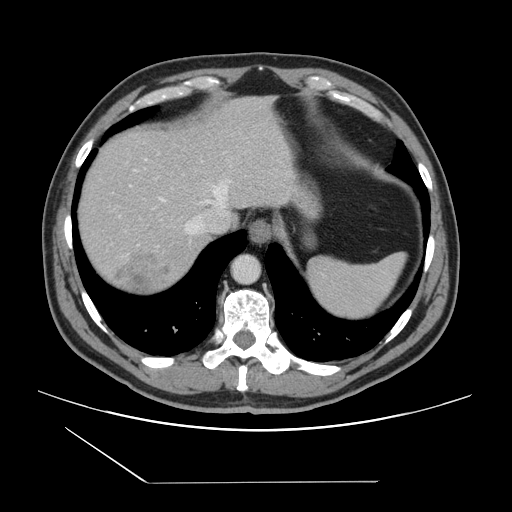
Contrast-enhanced abdominal CT, one axial slice. Position 123 of 157 along the scan axis. Intravenous contrast given. Soft-tissue window (W 400 / L 40 HU). 2.5 mm slice thickness. 512 × 512 image matrix, field of view 407 × 407 mm. Male patient, age 61 years. Case-level facts recorded for this patient, not image findings: diagnosis: colorectal cancer liver metastases, imaged before liver resection; multiple liver metastases: yes.
Outlined on this slice (expert manual segmentation):
- hepatic veins: bounding box [x1, y1, x2, y2] px = [160, 181, 228, 235]
- liver: [77, 96, 293, 296]
- planned liver remnant (the part of the liver to remain after resection): [78, 104, 233, 229]
- liver metastasis: [112, 250, 175, 294]